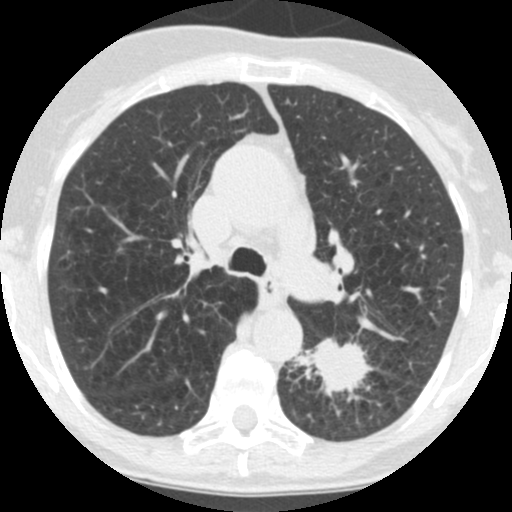
Axial slice from a low-dose chest CT screening exam. Third screening round (two years after baseline). Lung window (W 1500 / L -600 HU). Standard (soft-tissue) reconstruction kernel (STANDARD). Slice 55 of 171 in the series. 512 × 512 image matrix. Female participant, aged 71 years at enrolment. Current smoker at enrolment.
Expert reader's lesion annotation, box from (x=299, y=330) to (x=381, y=410) px. The screening reader recorded 2 non-calcified nodules or masses ≥4 mm on this exam; which of them this box marks is not recorded. Official screen result: positive, other. Participant outcome: lung cancer diagnosed 26 days after this screen — squamous cell carcinoma, NOS, left lower lobe, poorly differentiated (G3), stage IB (AJCC 6th edition), 40 mm at pathology.